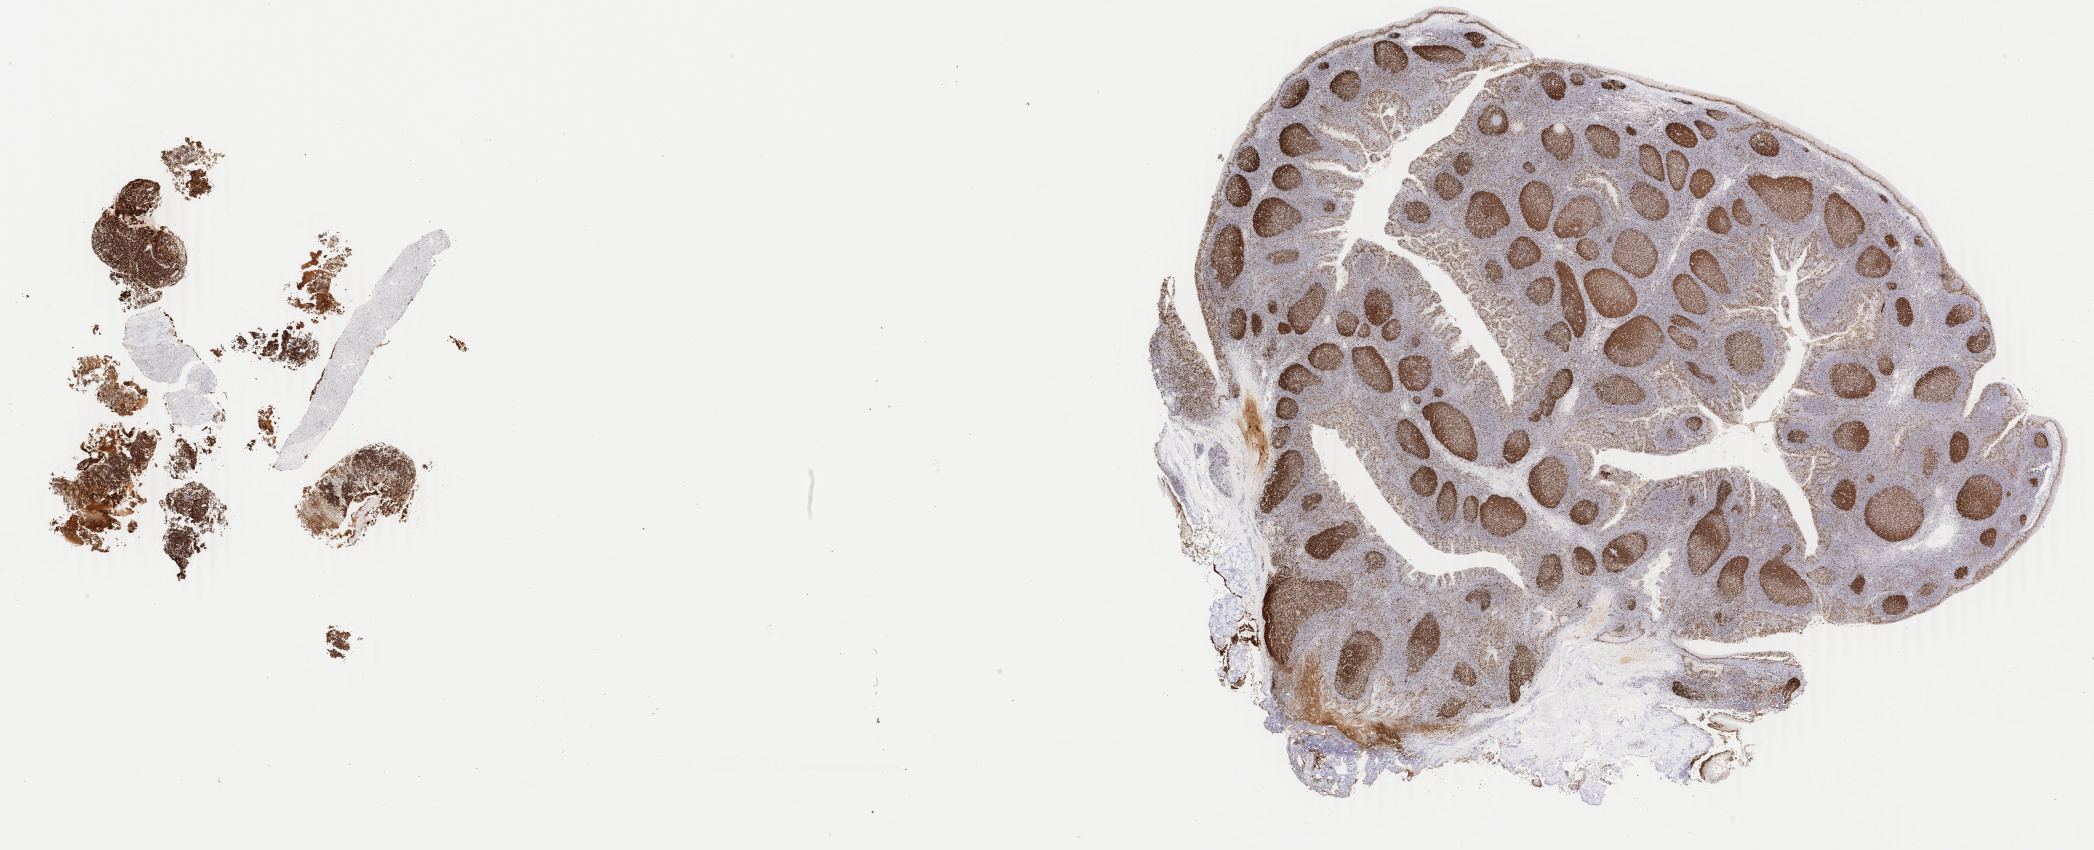
Whole-slide image, immunohistochemical stain for Ki-67 — a low-resolution overview of the entire scanned area, about 33.3 x 13.5 mm, specimen: tumor tissue, site: liver. Male patient; age at initial diagnosis 5 years.
* histologic diagnosis: Burkitt lymphoma, NOS